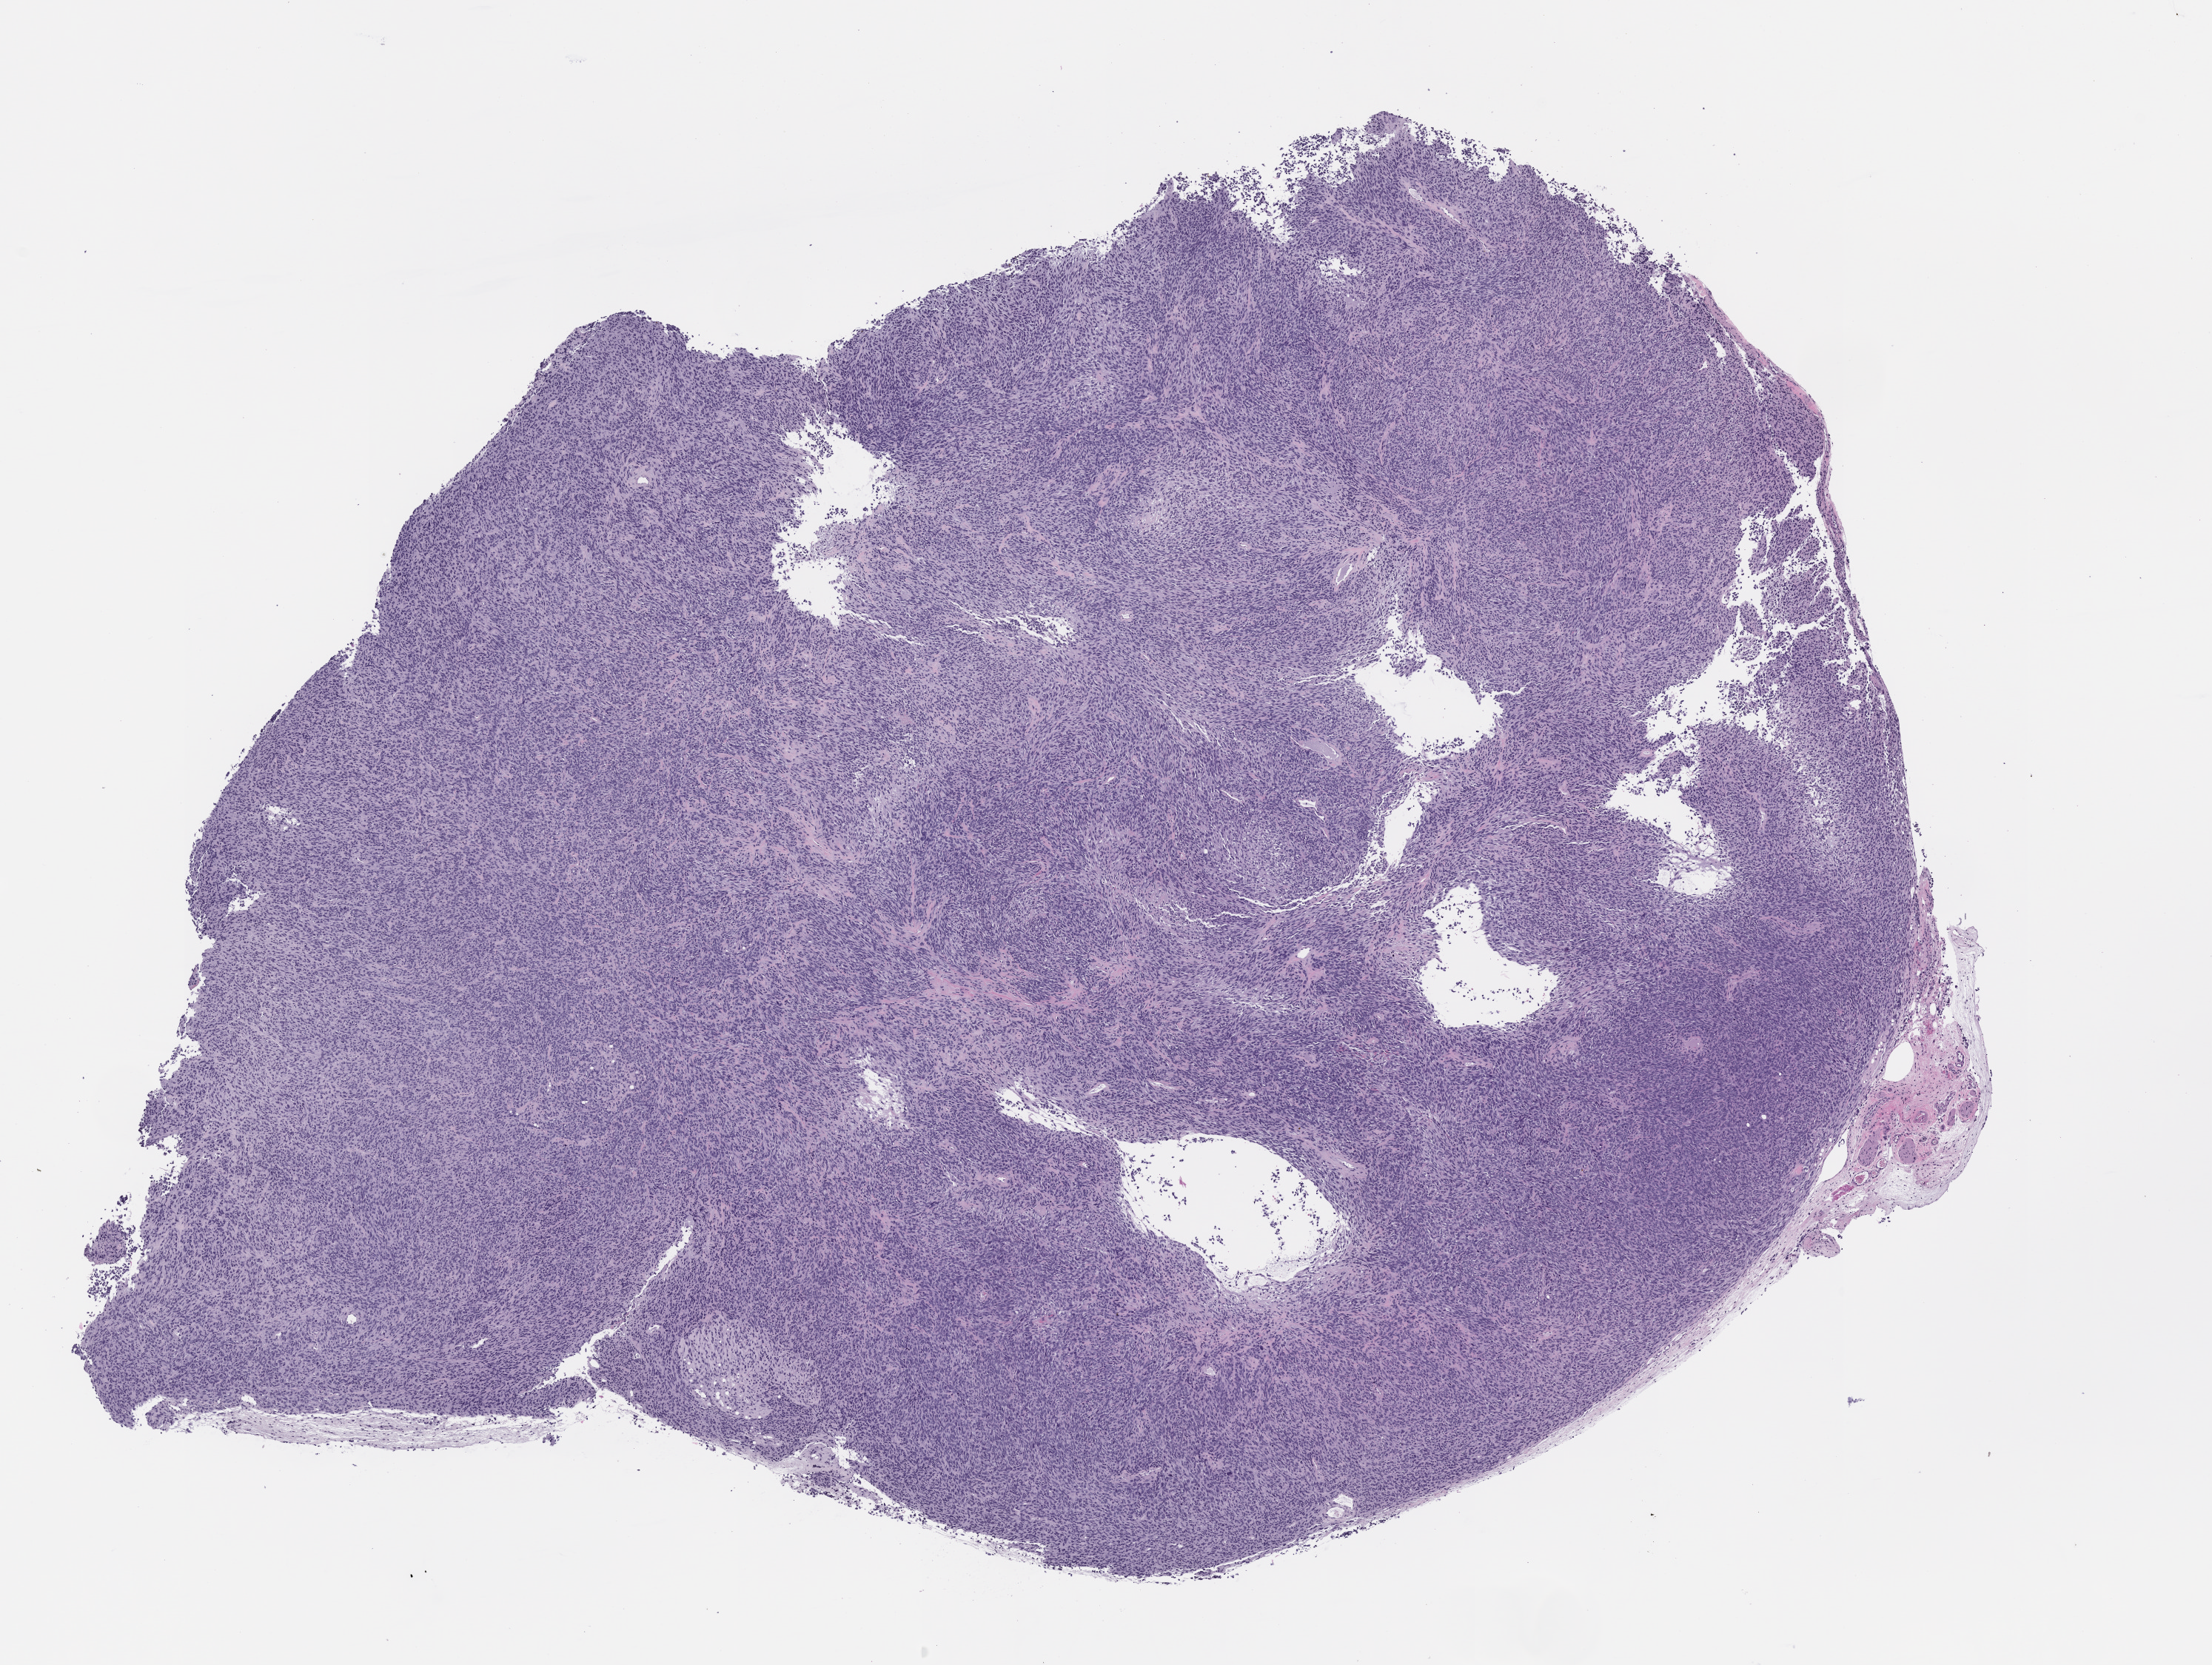
Haematoxylin and eosin whole-slide image of a patient-derived xenograft (PDX) tumor grown in a mouse, passage 1, low-resolution overview of the scanned area, about 12.0 x 9.0 mm; formalin-fixed, paraffin-embedded (FFPE) tissue; tumor site category: musculoskeletal.
Originating patient diagnosis: Spindle Cell Sarcoma.